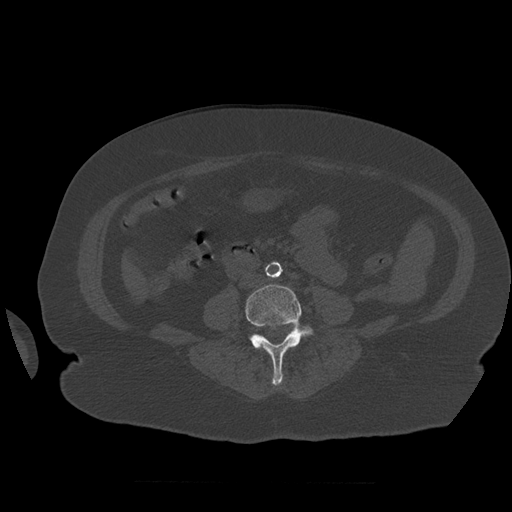
CT including the spine, one axial slice. Position 204 of 399 along the scan axis. Bone window (W 1800 / L 400 HU). 512 × 512 image matrix. Patient age 81 years. From the clinical record (not read from this slice): primary cancer: renal.
Annotated regions visible in this slice (semi-automatically segmented with operator editing):
- L4 vertebra: bounding box (x1, y1, x2, y2) in pixels: (246, 284, 314, 386)